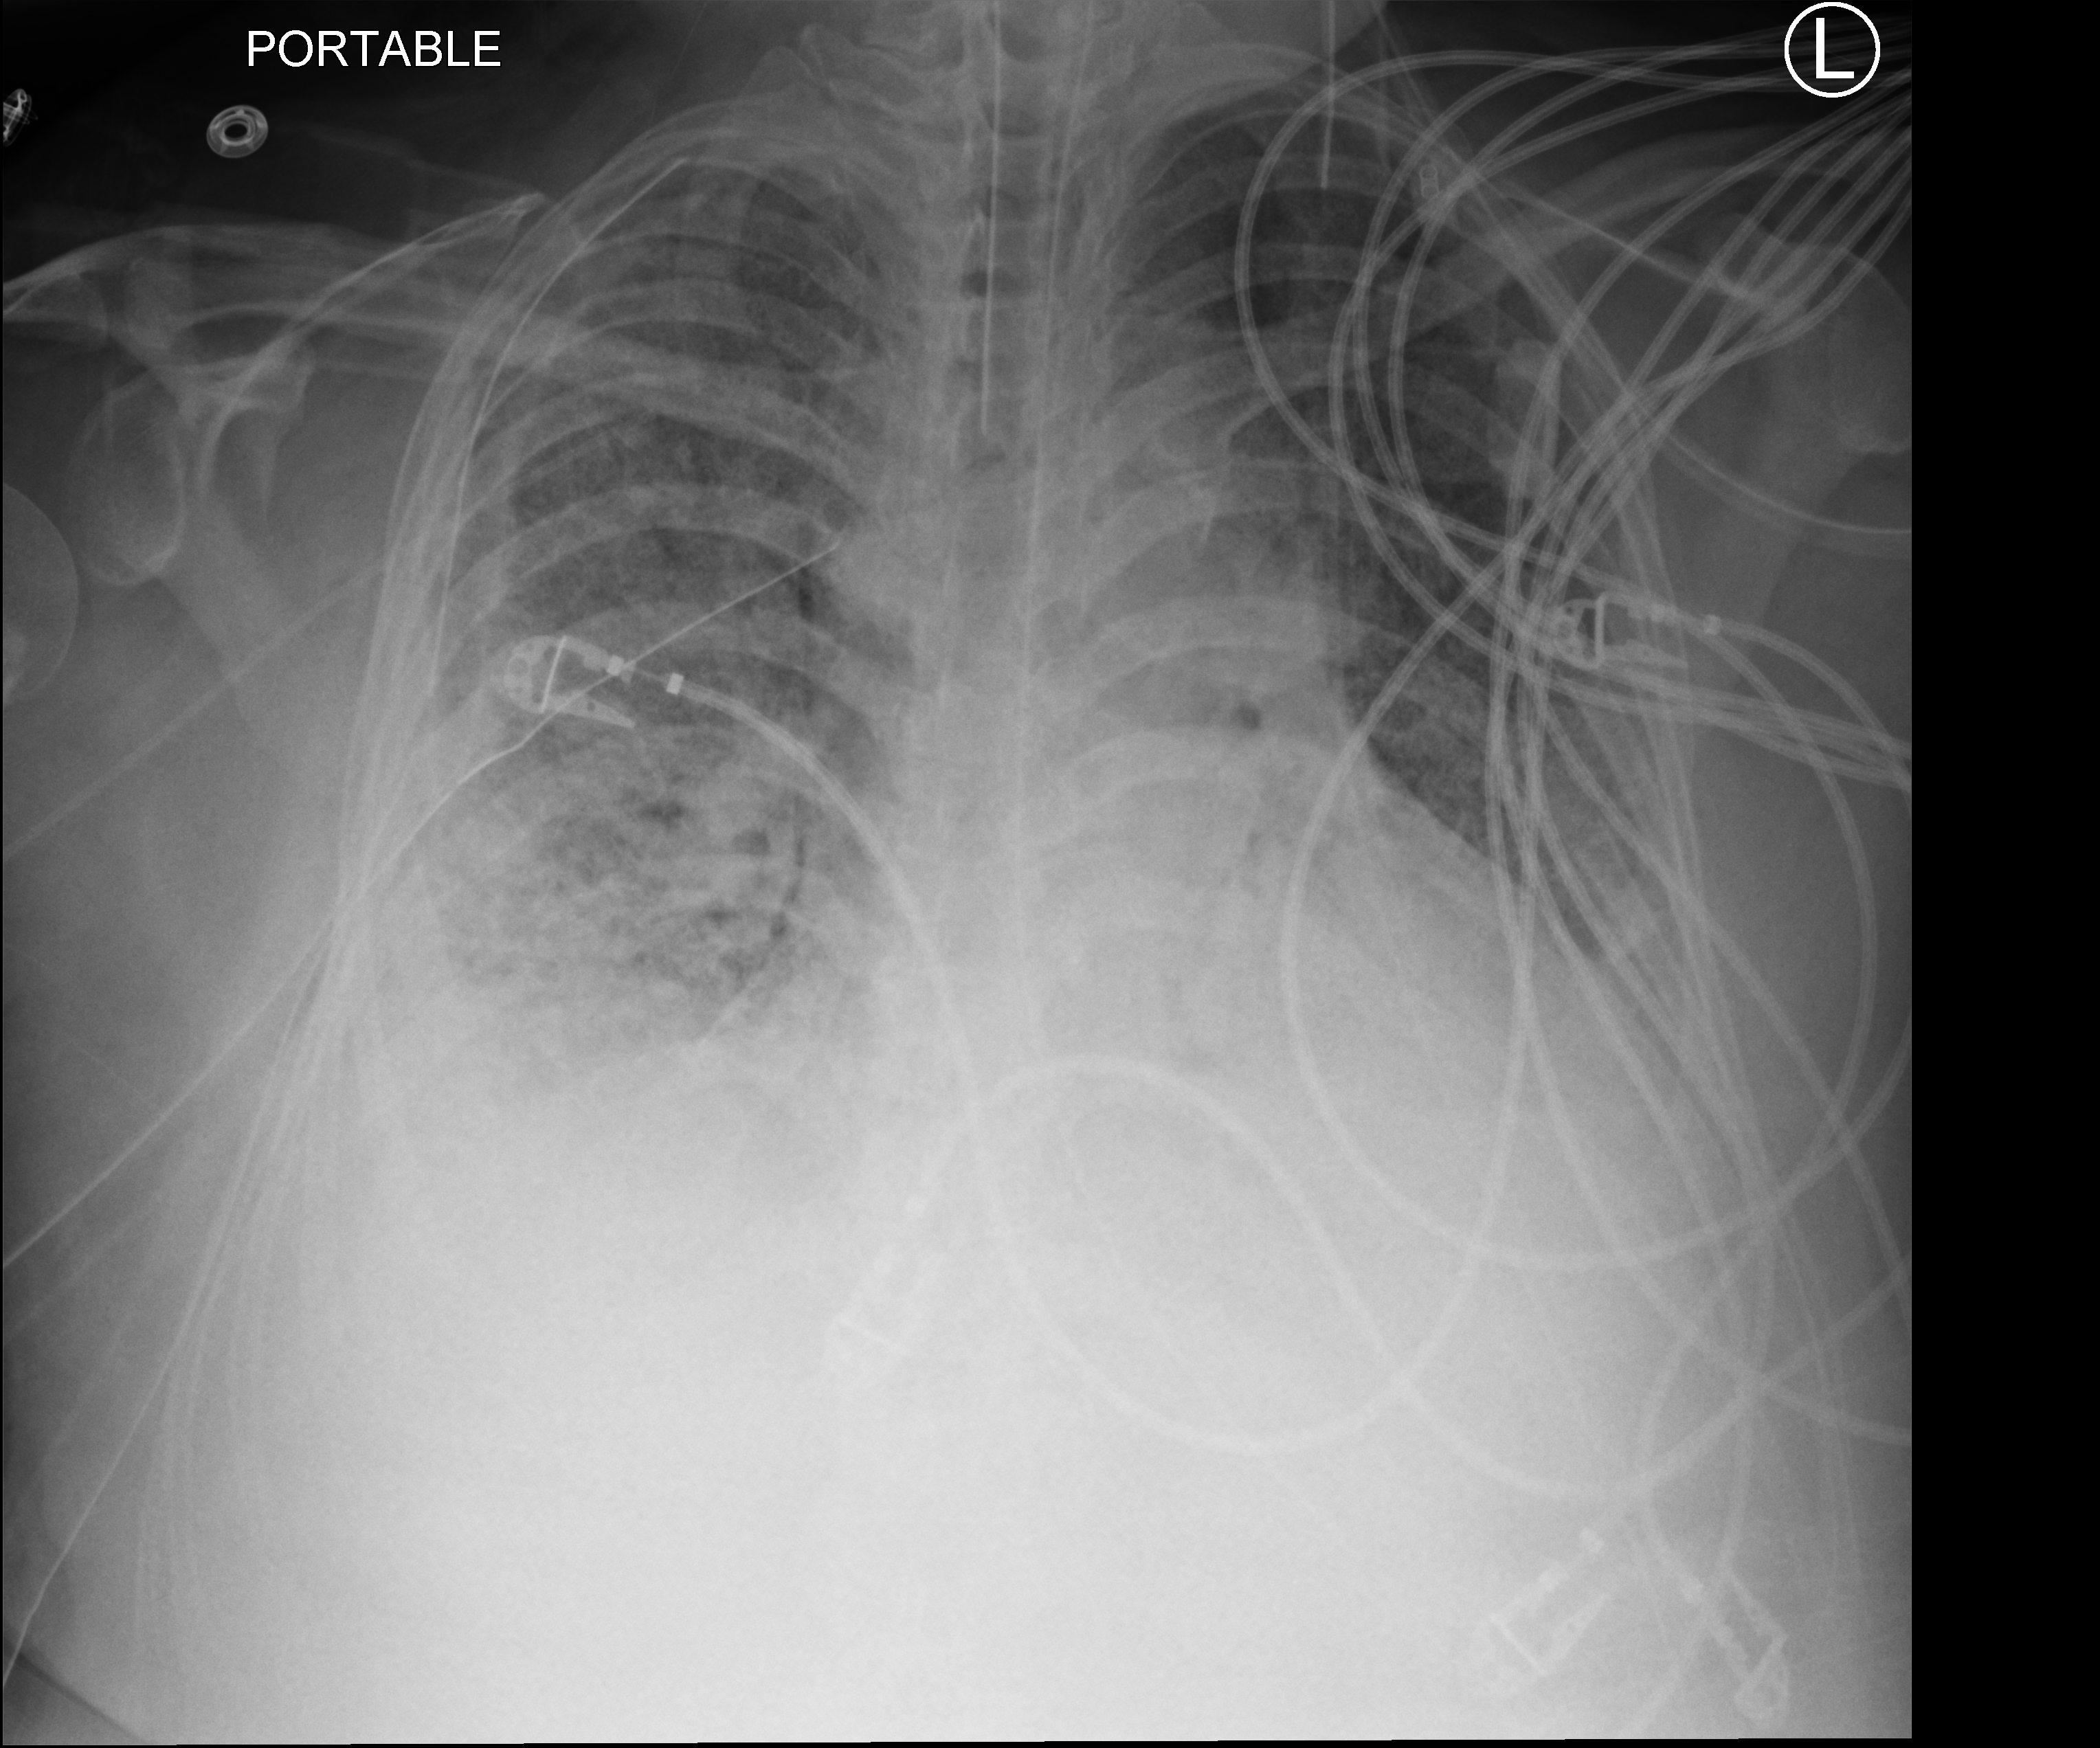
Portable chest radiograph. Adult patient hospitalised with COVID-19, age 18–59 years.
Hospital-stay facts (about this admission, not read from this image; timing relative to this image not recorded):
- mechanically ventilated during this hospital stay: yes
- admitted to intensive care during this hospital stay: yes